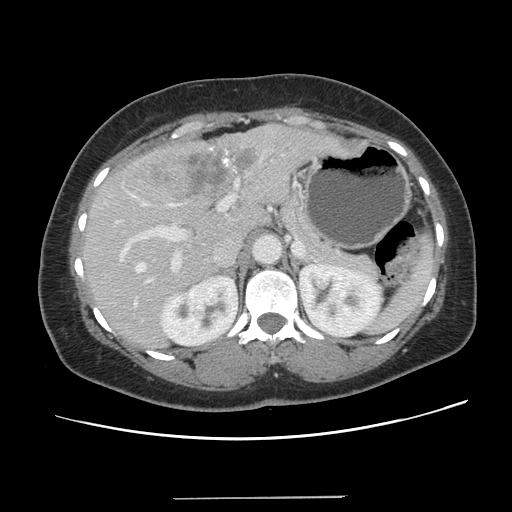
Contrast-enhanced abdominal CT, one axial slice. Position 84 of 141 along the scan axis. 120 kVp. Intravenous contrast given. Soft-tissue window (W 400 / L 40 HU). 2.5 mm slice thickness. 512 × 512 image matrix. Female patient, age 53 years. From the clinical record (not read from this slice): diagnosis: colorectal cancer liver metastases, imaged before liver resection; multiple liver metastases: no; largest metastasis: 14.5 cm; chemotherapy before resection: yes.
Outlined on this slice (expert manual segmentation):
- hepatic veins: bounding box (x1, y1, x2, y2) in pixels: (134, 202, 176, 304)
- liver: (83, 126, 347, 348)
- planned liver remnant (the part of the liver to remain after resection): (84, 206, 263, 349)
- portal vein (with intrahepatic branches): (120, 180, 238, 285)
- liver metastasis: (144, 147, 258, 199)